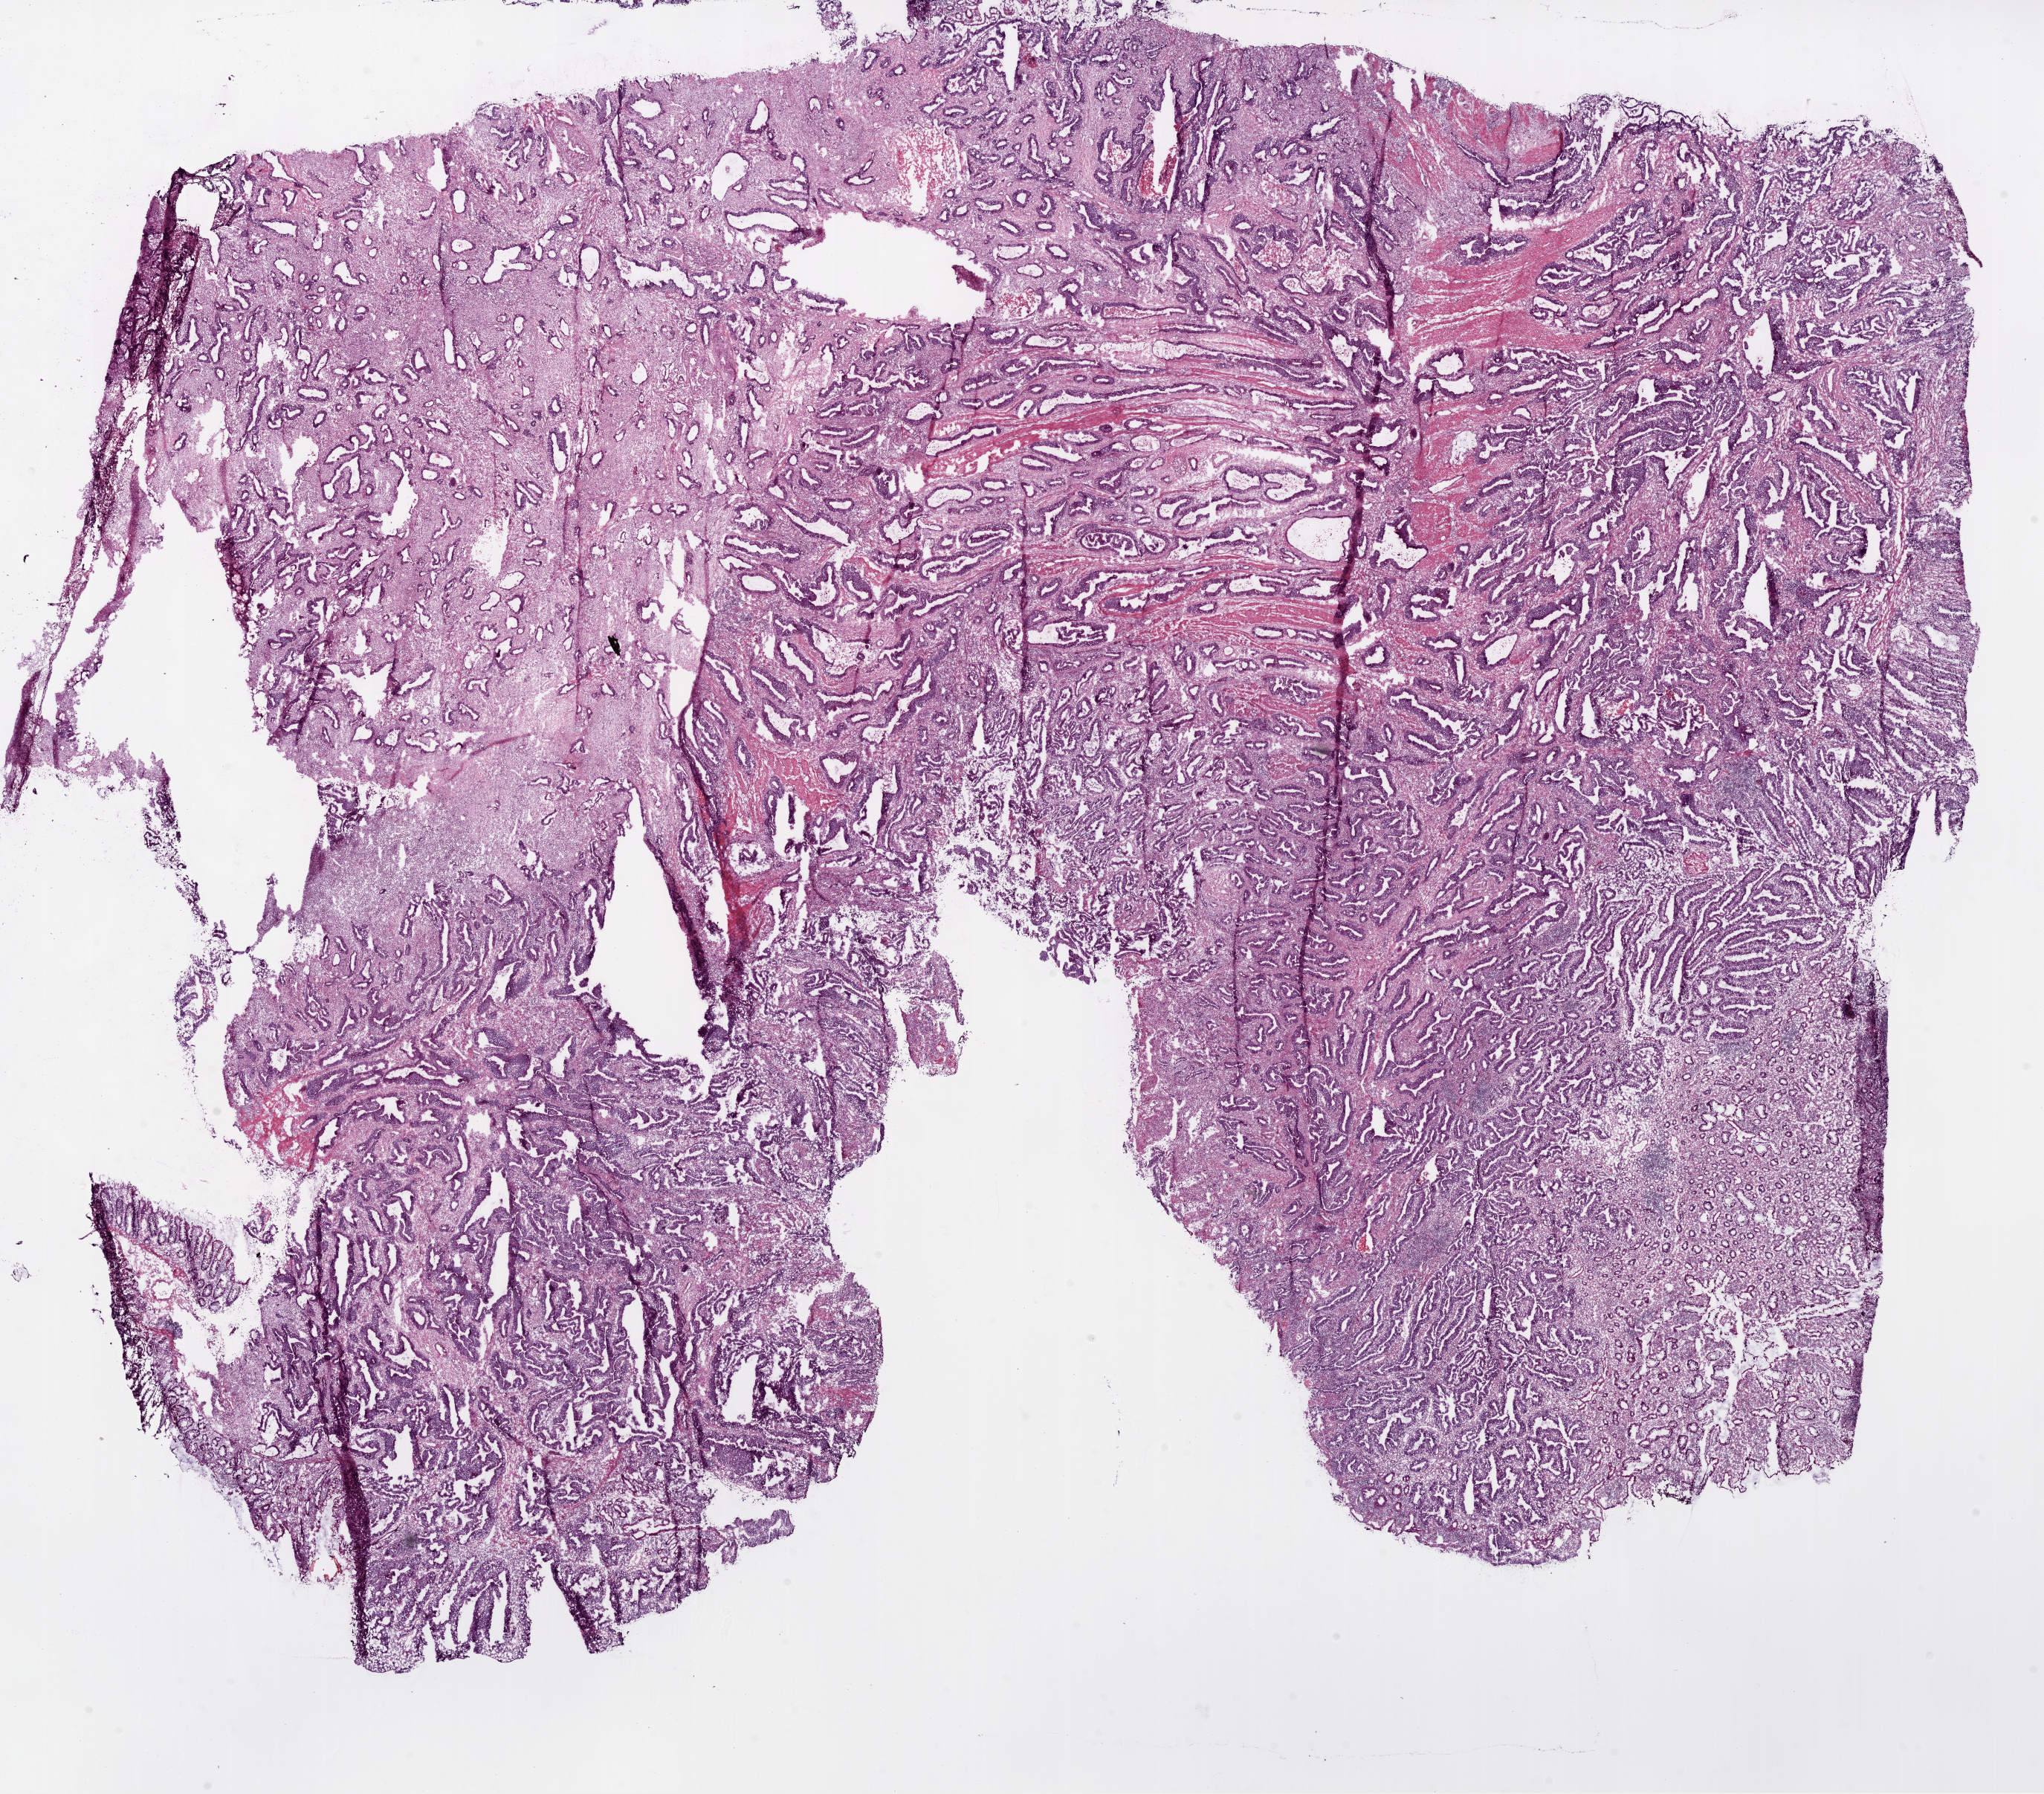
Digitized H&E tissue section (whole slide), a low-resolution overview of the entire scanned area, about 22.1 x 19.4 mm; frozen section; colon, primary tumour sample. Patient: male, age at initial diagnosis 47 years. Slide review estimates, as recorded: tumour cells 77%, tumour nuclei 75%, normal cells 5%, stromal cells 15%, necrosis 3%.
Lymph nodes positive (case pathology): 2 of 29 examined. Histologic diagnosis: Adenocarcinoma, NOS. AJCC pathologic stage: IVA.